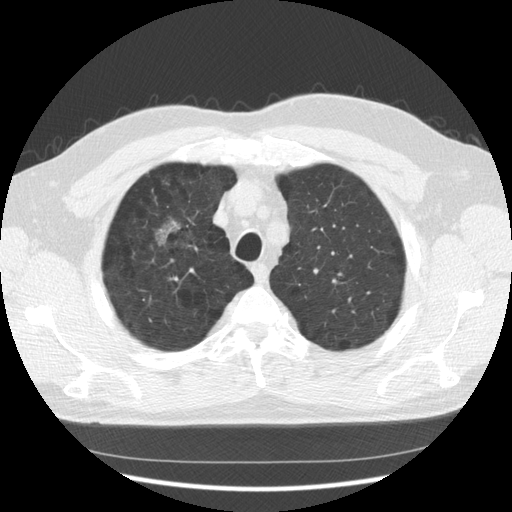
Low-dose screening chest CT, axial slice, third screening round (two years after baseline), lung window (W 1500 / L -600 HU), 2.5 mm slice thickness, 140 kVp, slice 101 of 133 in the series. Male participant, aged 60 years at enrolment.
Lesion marked by an expert reader, box from (x=143, y=208) to (x=198, y=265) px. The exam's reader record, not a measurement of the box and not confirmed to be the same lesion: non-calcified nodule or mass ≥4 mm, right upper lobe, poorly defined margins, mixed attenuation, pre-existing on the prior screen: yes; interval growth: yes. Participant outcome: lung cancer diagnosed 121 days after this screen — papillary adenocarcinoma, NOS, right upper lobe, moderately differentiated (G2), stage IB (AJCC 6th edition), 32 mm at pathology.